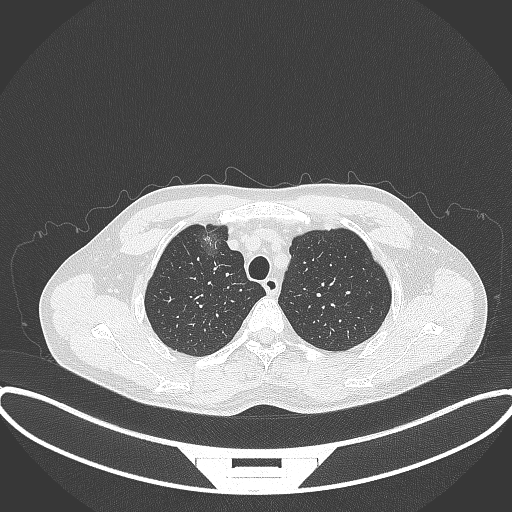
Chest CT, one axial slice. Slice 298 of 395 in the series (ordered by position). Reconstruction kernel B70f. Lung window (W 1500 / L -600 HU). 1 mm slice thickness. 512 × 512 image matrix, field of view 424 × 424 mm. Male patient, age 60 years. From the clinical record (not read from this slice): clinical TNM (as recorded): T1c N0 M0.
Outlined on this slice (bounding box drawn by a radiologist):
- lung tumour (recorded histology: adenocarcinoma): bounding box [x1, y1, x2, y2] px = [193, 221, 229, 265]